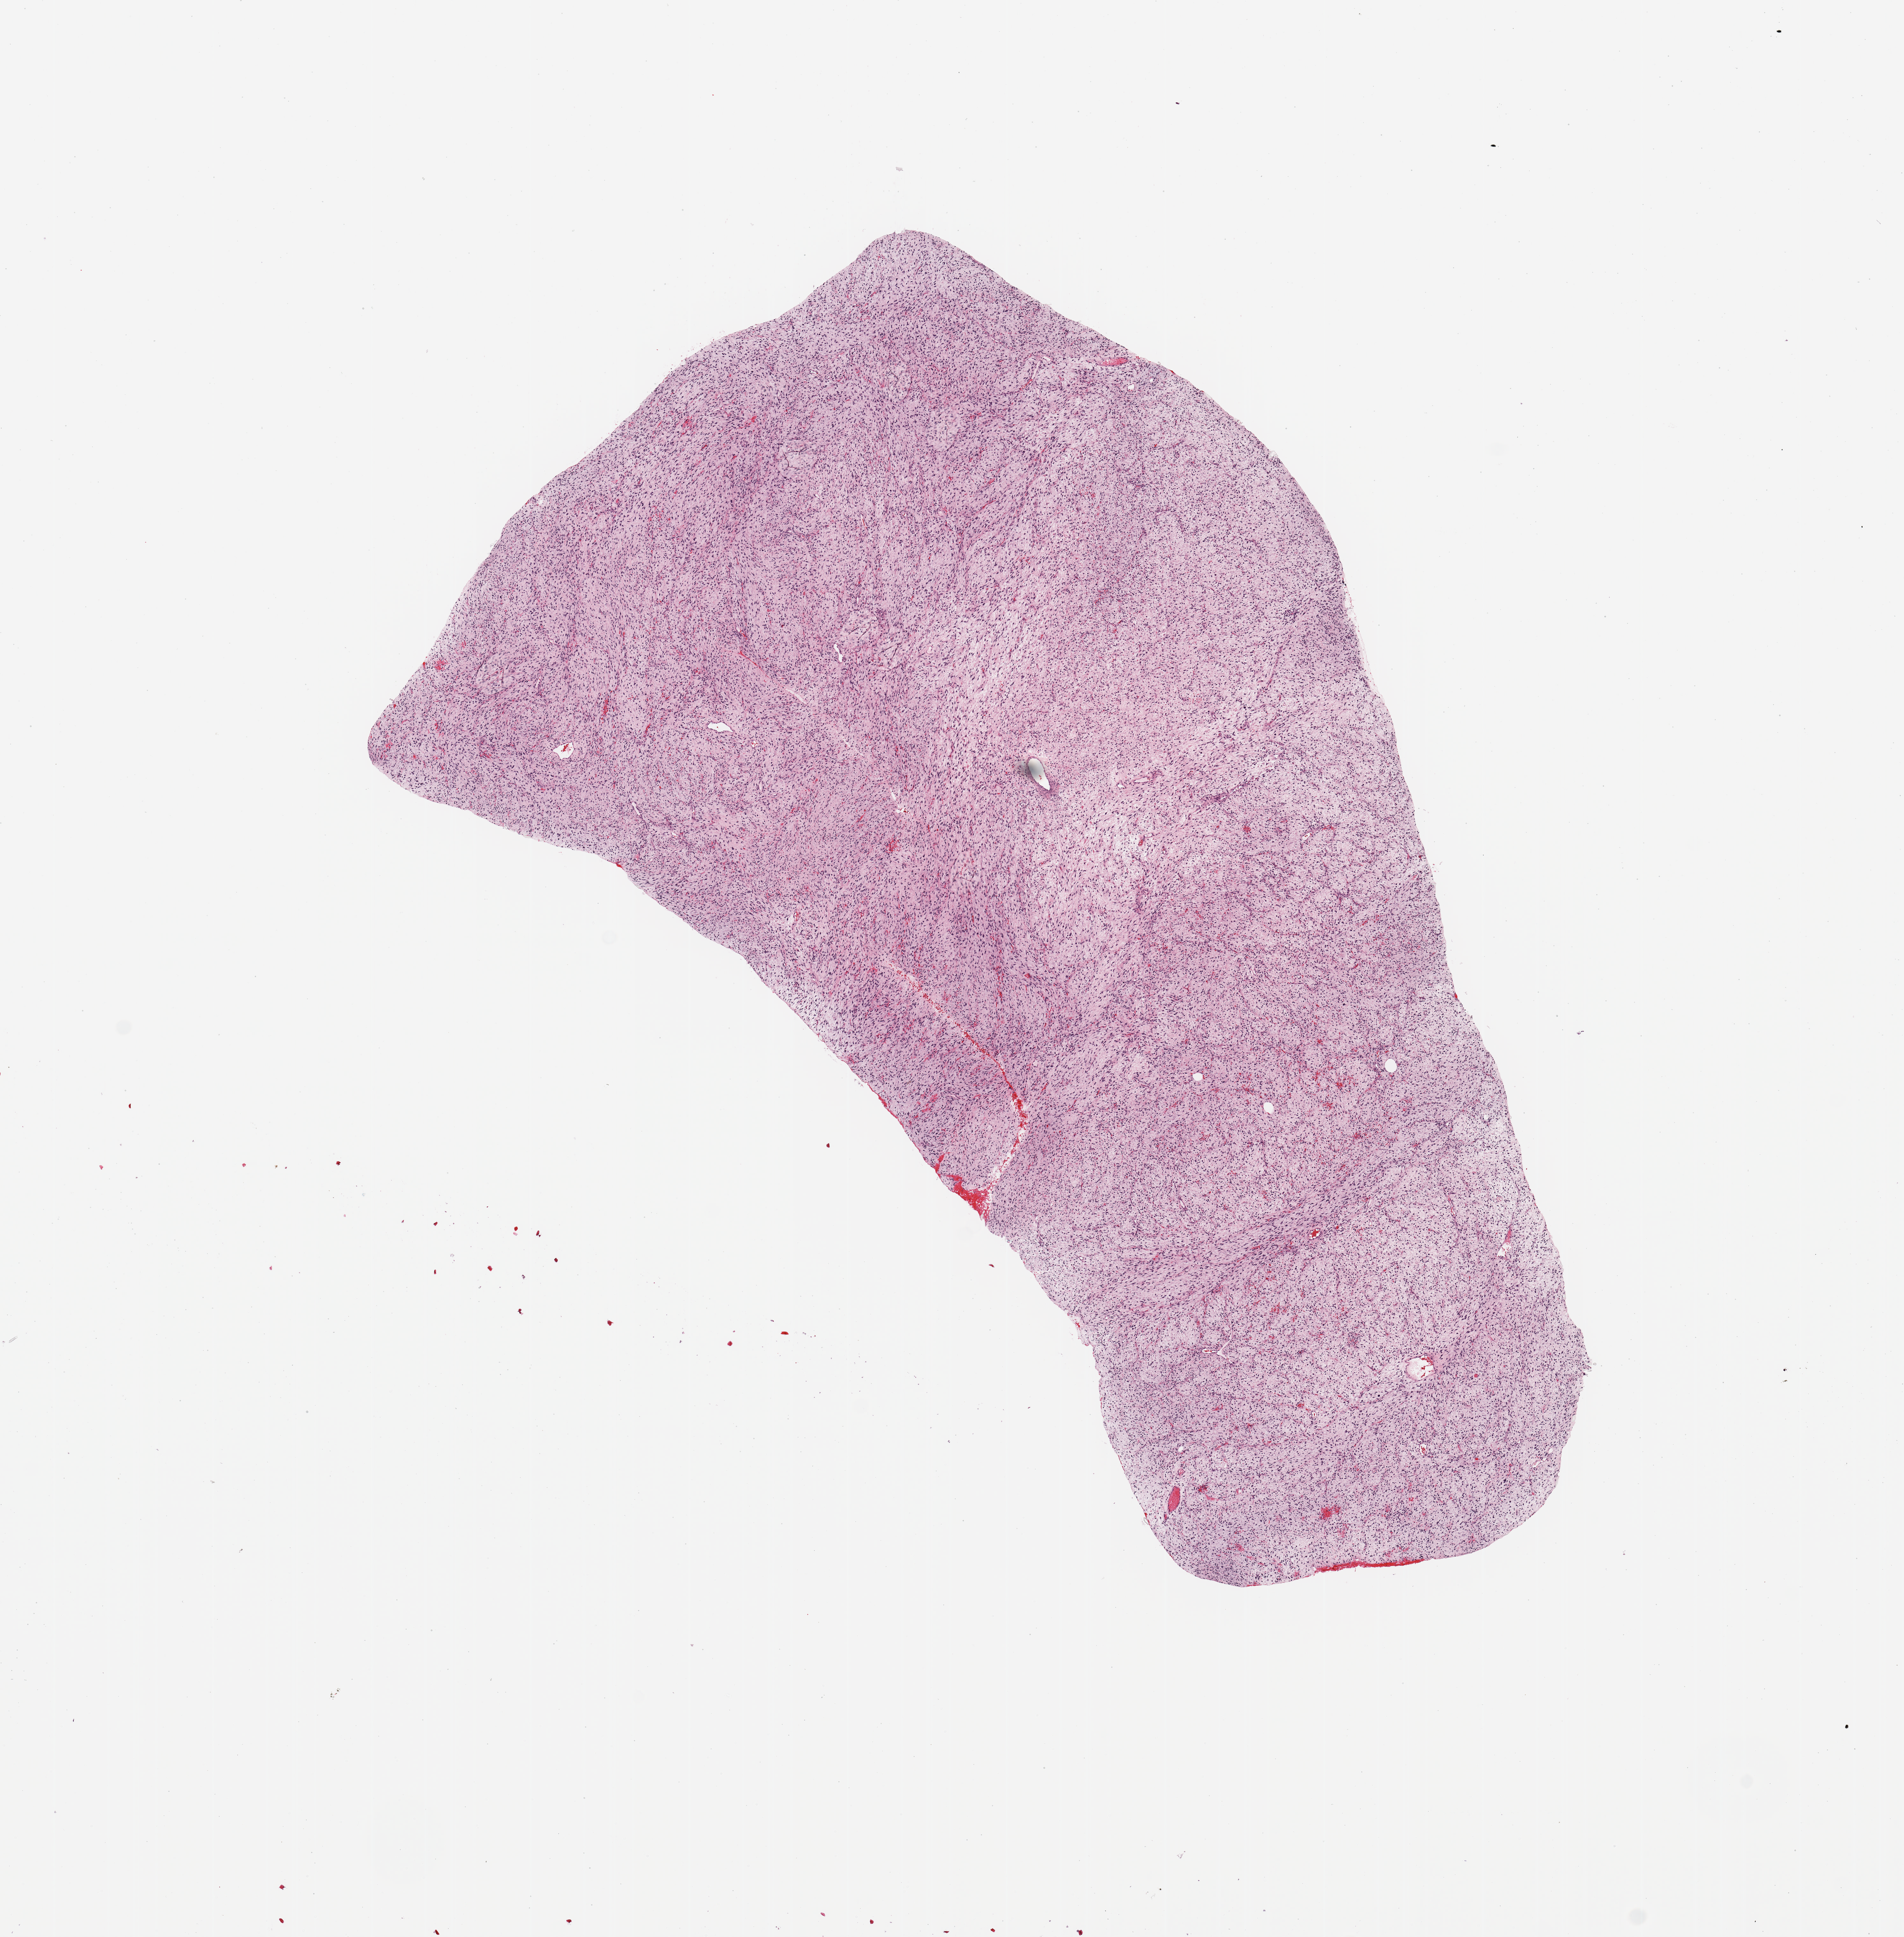
Digitized H&E-stained tissue section (whole slide) — shown as a low-resolution overview of the whole scanned area (about 11.8 x 12.0 mm), tumour tissue sample. Male patient.
- patient diagnosis (cohort enrolment): sarcoma (site not recorded at cohort level)